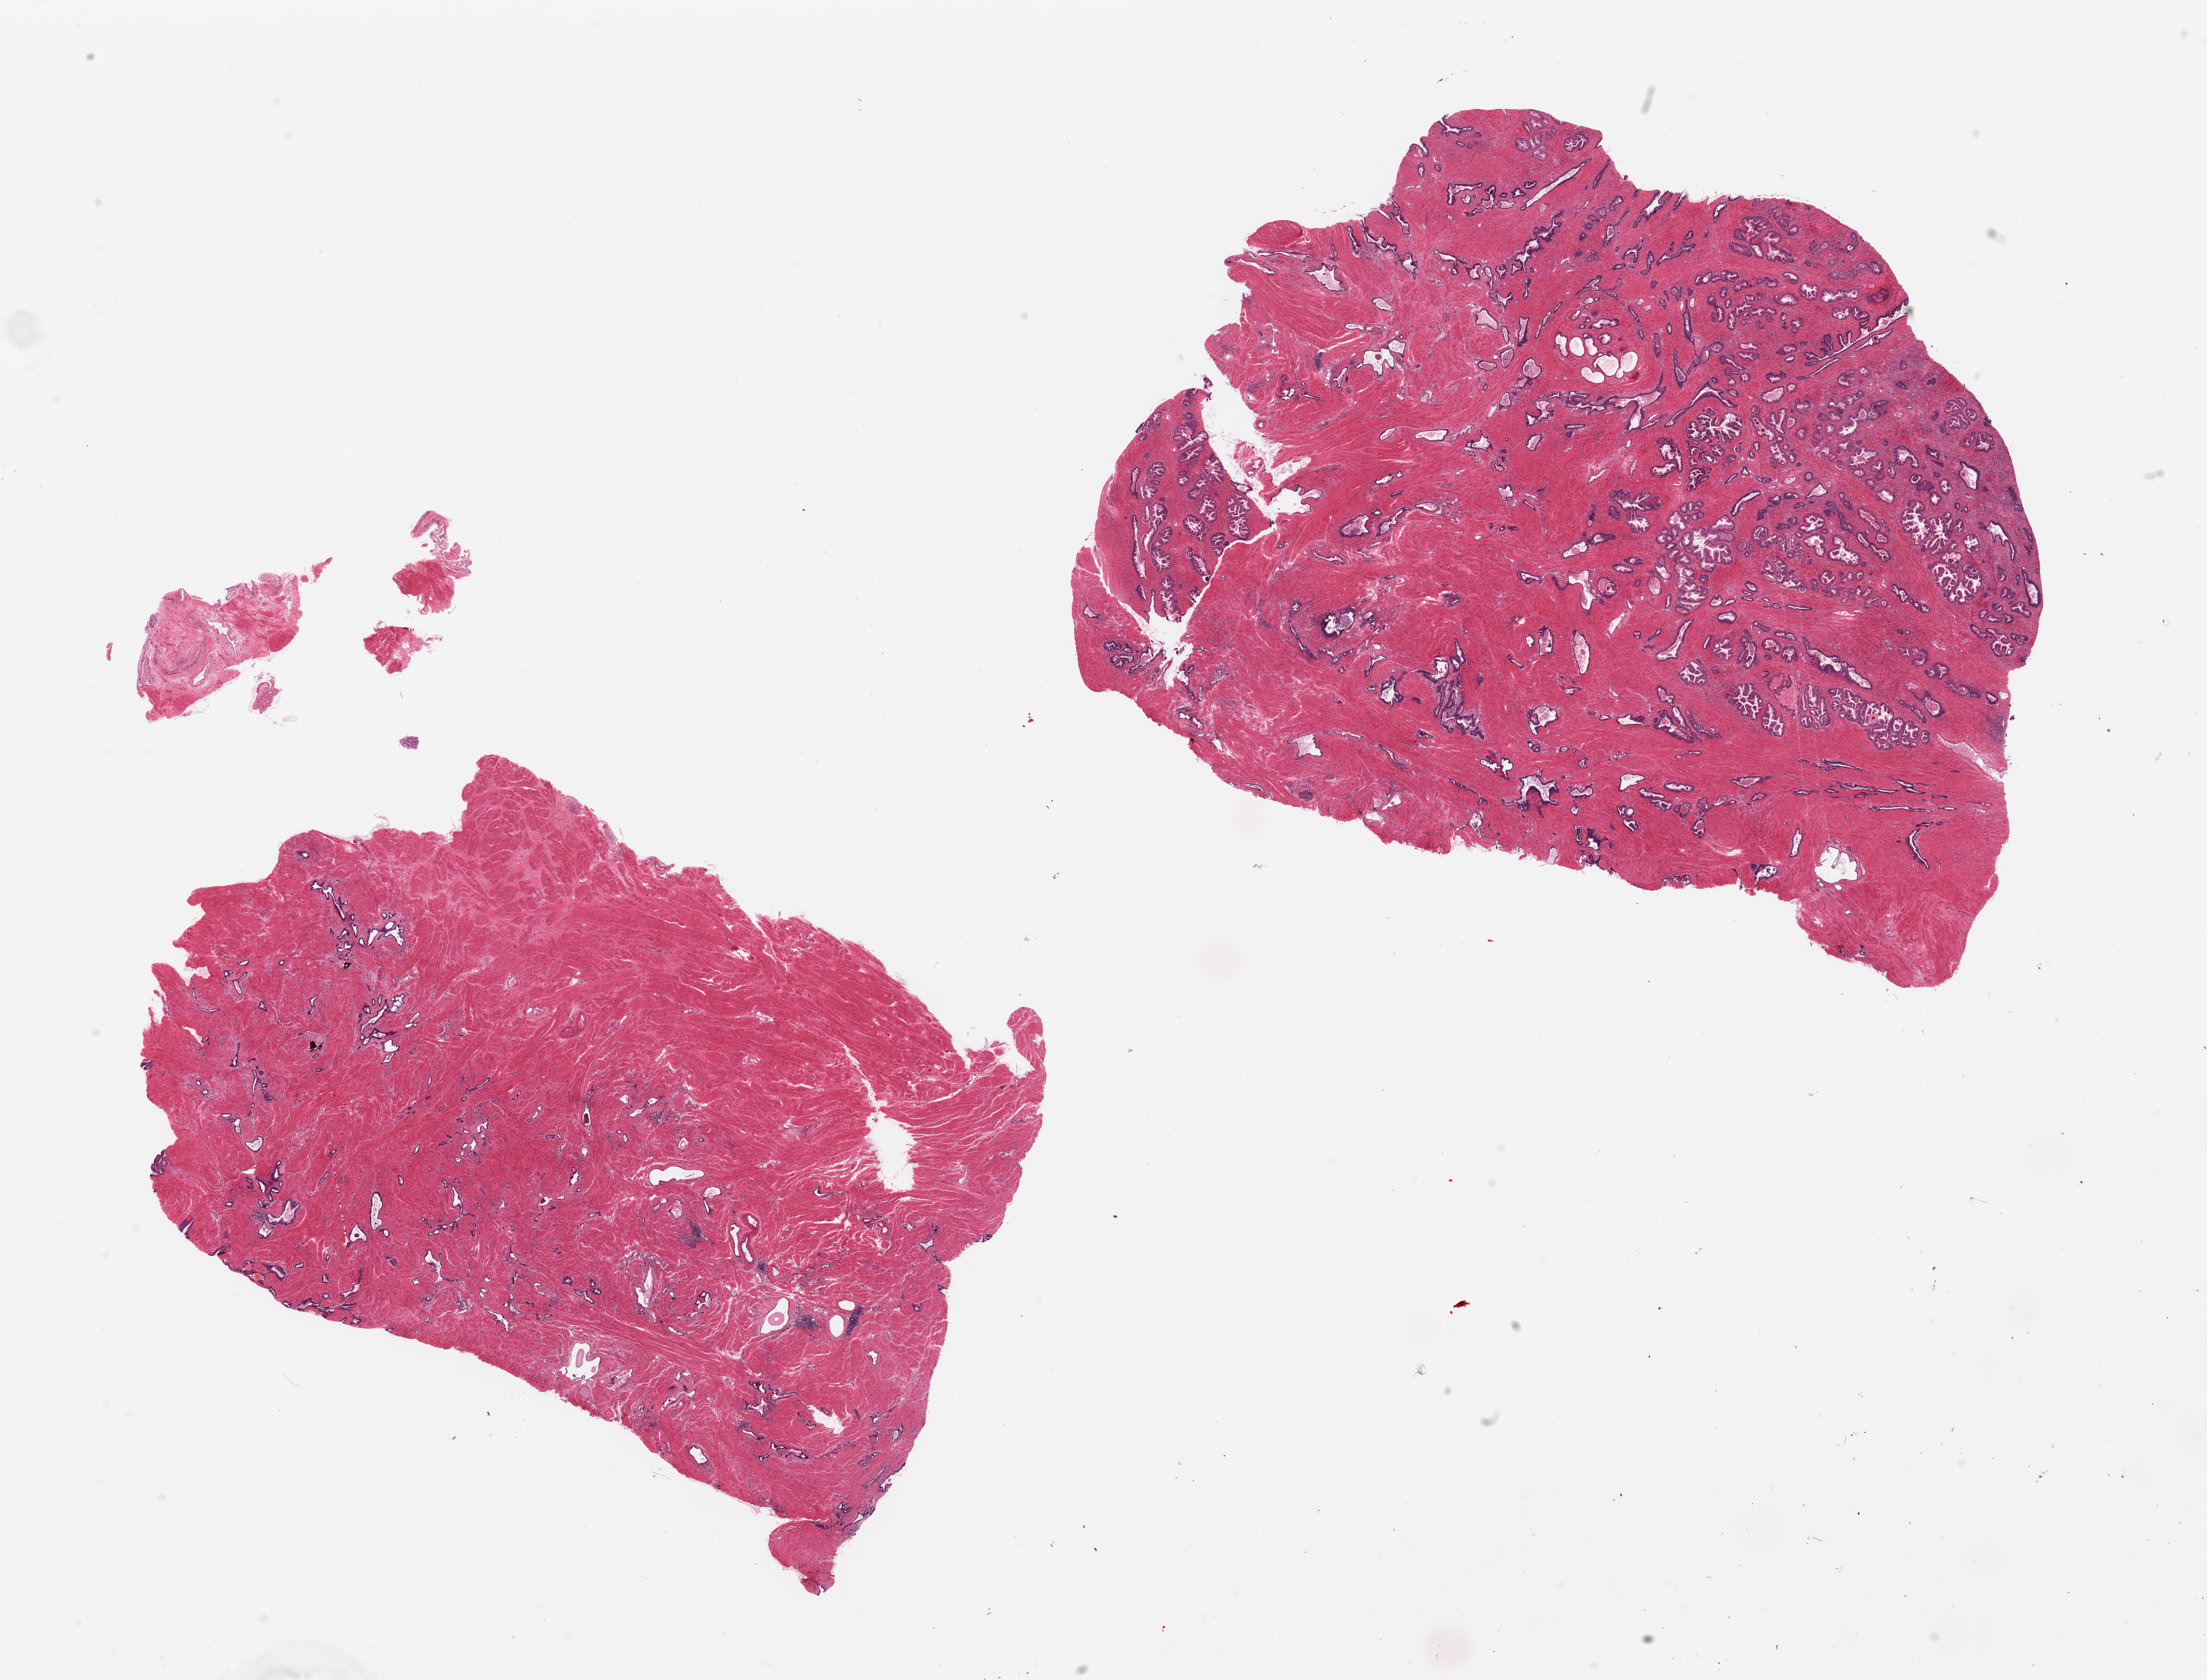
Haematoxylin and eosin whole-slide image, shown as a low-resolution overview of the whole scanned area (about 28.5 x 21.7 mm, acquisition: 20x scan); PAXgene-fixed, paraffin-embedded tissue; target tissue: prostate; donor tissue sample. Donor: male.
Review note (as recorded): 2 pieces, glandular epithelial hyperplasia, well -preserved.